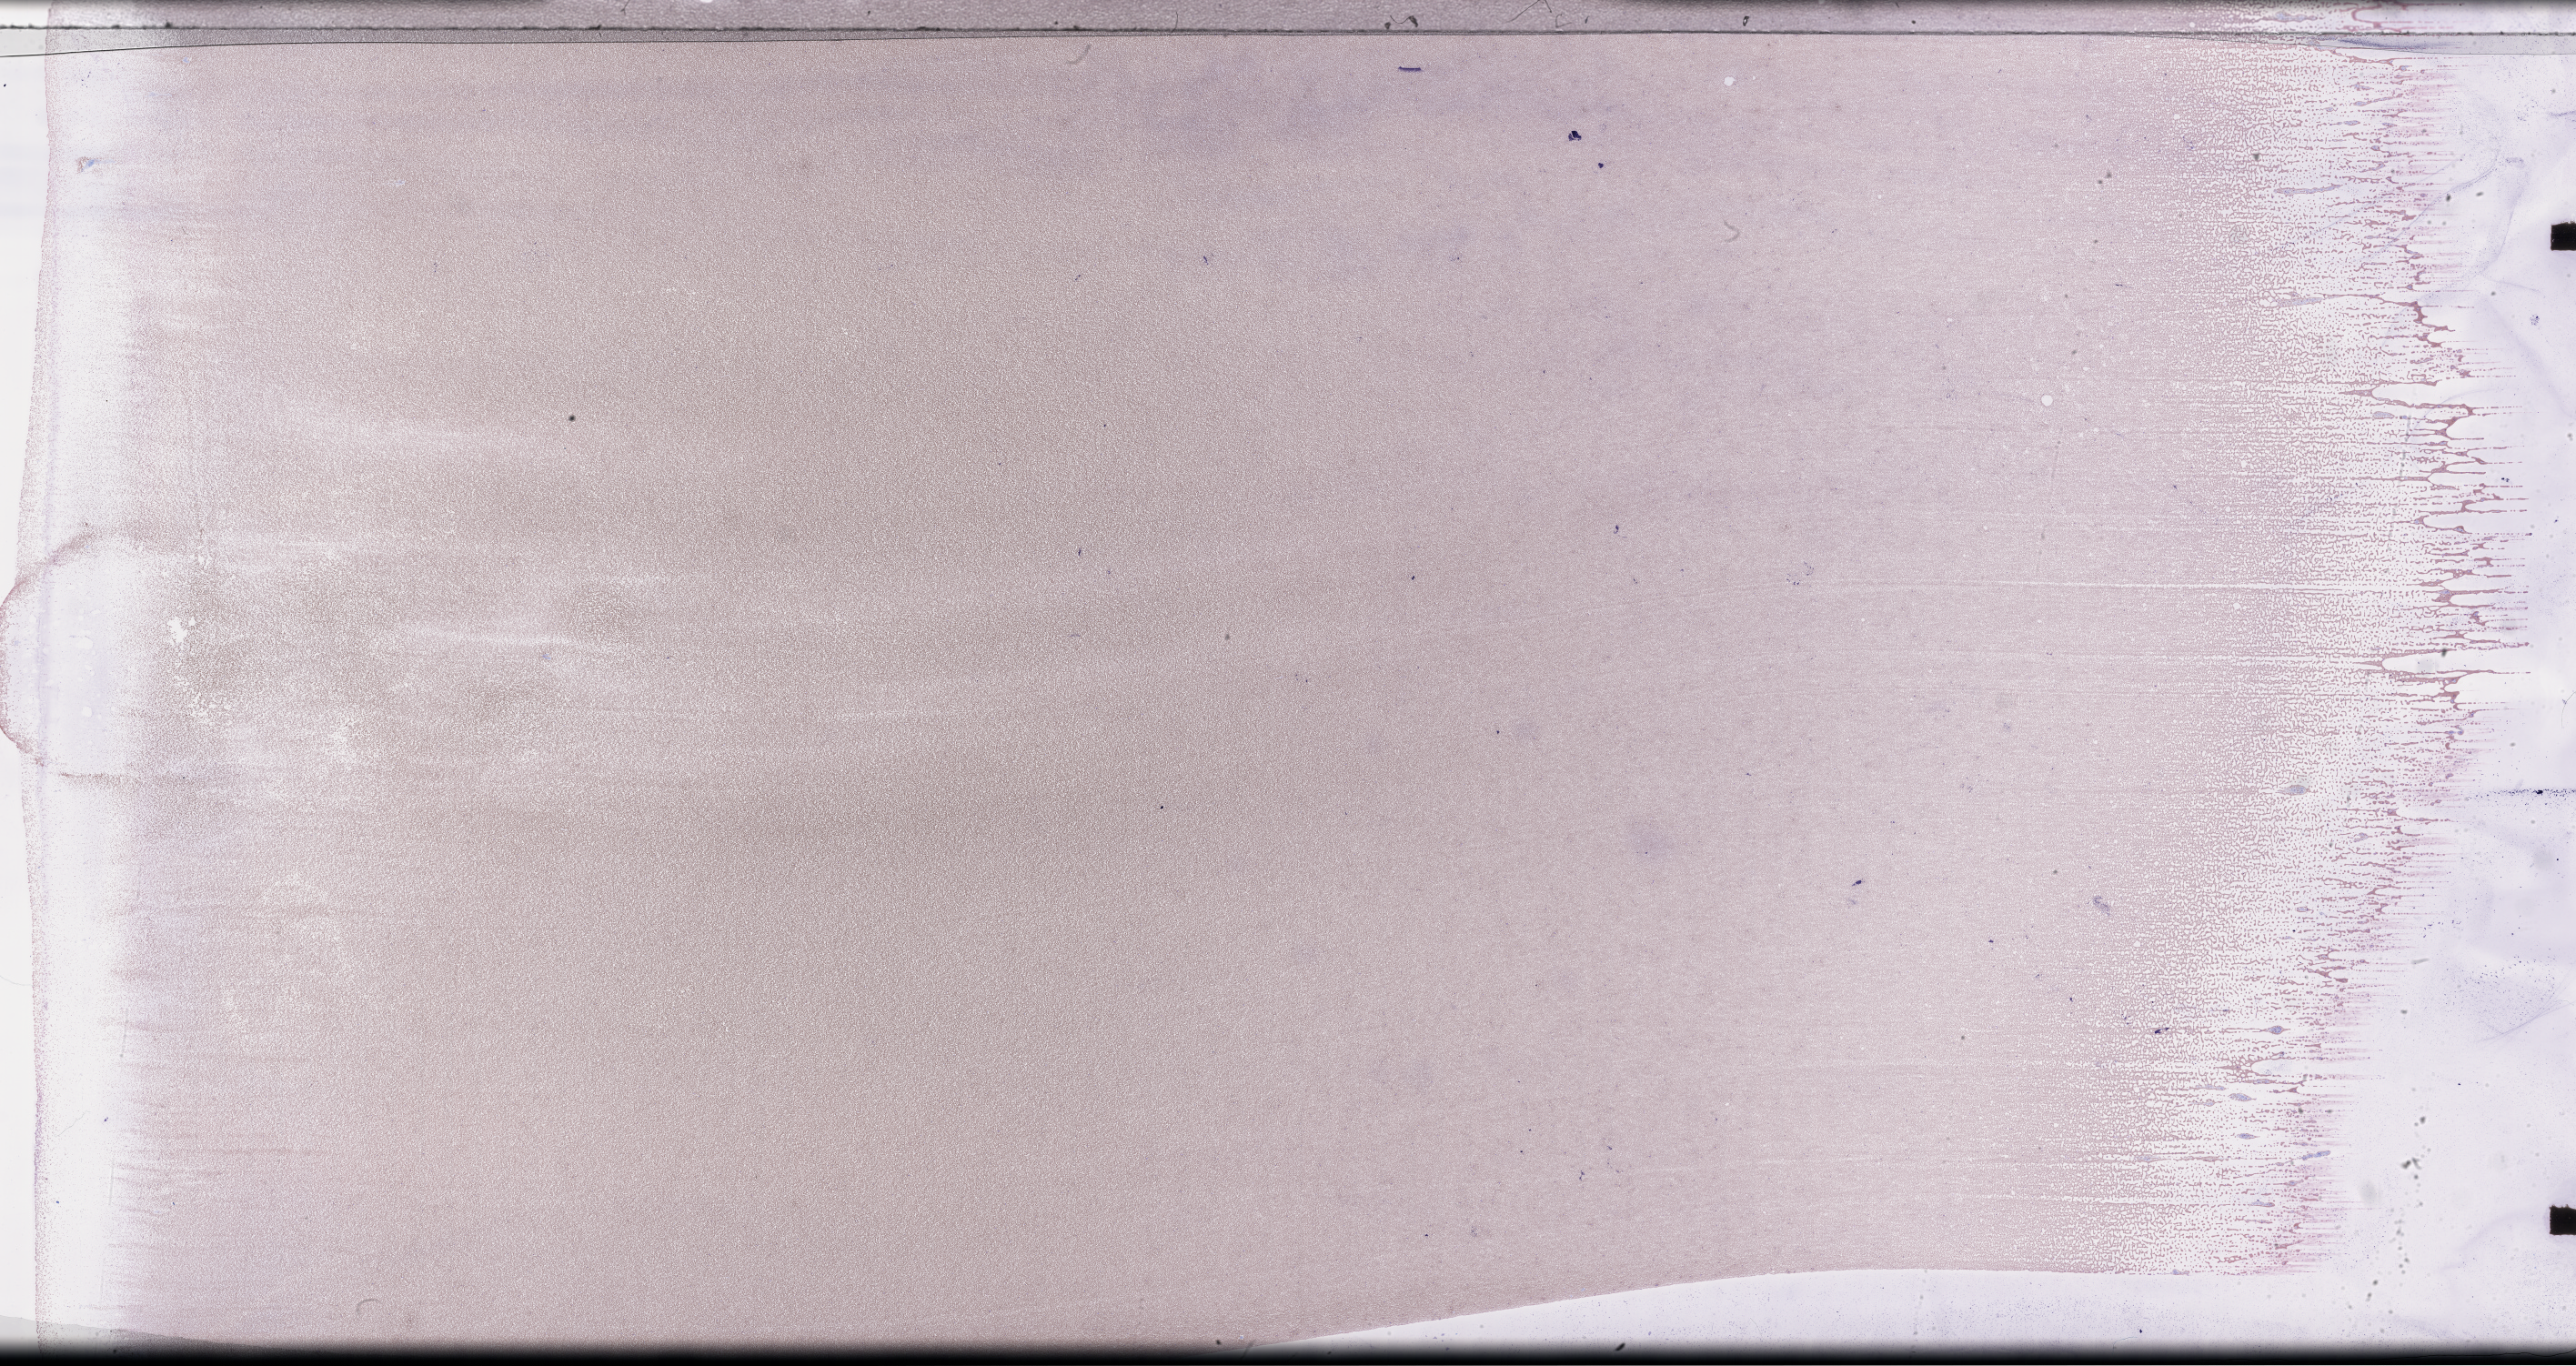
Wright-Giemsa-stained whole blood smear, whole-slide image — a low-resolution overview of the entire scanned area, about 45.7 x 24.3 mm. Smear from an EDTA sample. Specimen time point: collected on treatment. Male patient.
* from a patient with: Plasma Cell Myeloma